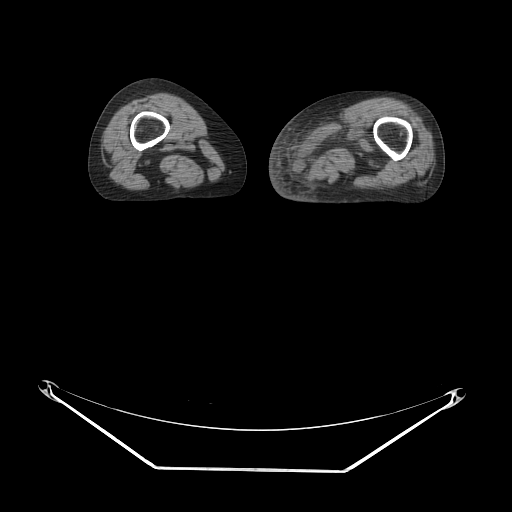
CT of an extremity soft-tissue mass (from a PET/CT study), one axial slice. Slice 9 of 91 in the series (ordered by position). 140 kVp. Soft-tissue window (W 400 / L 40 HU). 3.75 mm slice thickness. 512 × 512 image matrix. Female patient. From the clinical record (not read from this slice): histological type: pleomorphic leiomyosarcoma; grade: high; site of the primary tumour: left thigh.
Annotated regions visible in this slice (expert contour drawn on MRI and transferred to this co-registered scan by the dataset authors):
- gross tumour volume including surrounding oedema: bounding box (x1, y1, x2, y2) in pixels: (301, 112, 382, 179)